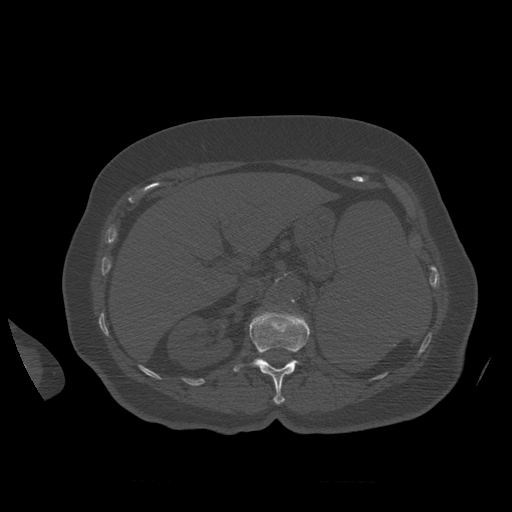
CT including the spine, one axial slice; position 275 of 399 along the scan axis; reconstruction kernel STANDARD; bone window (W 1800 / L 400 HU); 512 × 512 image matrix, field of view 404 × 404 mm. Patient age 81 years. From the clinical record (not read from this slice): primary cancer: renal; vertebrae with lytic lesions (as recorded): L1.
Annotated regions visible in this slice (semi-automatic segmentation, software-assisted and operator-edited):
- L1 vertebra: box from (x=234, y=309) to (x=310, y=405) px